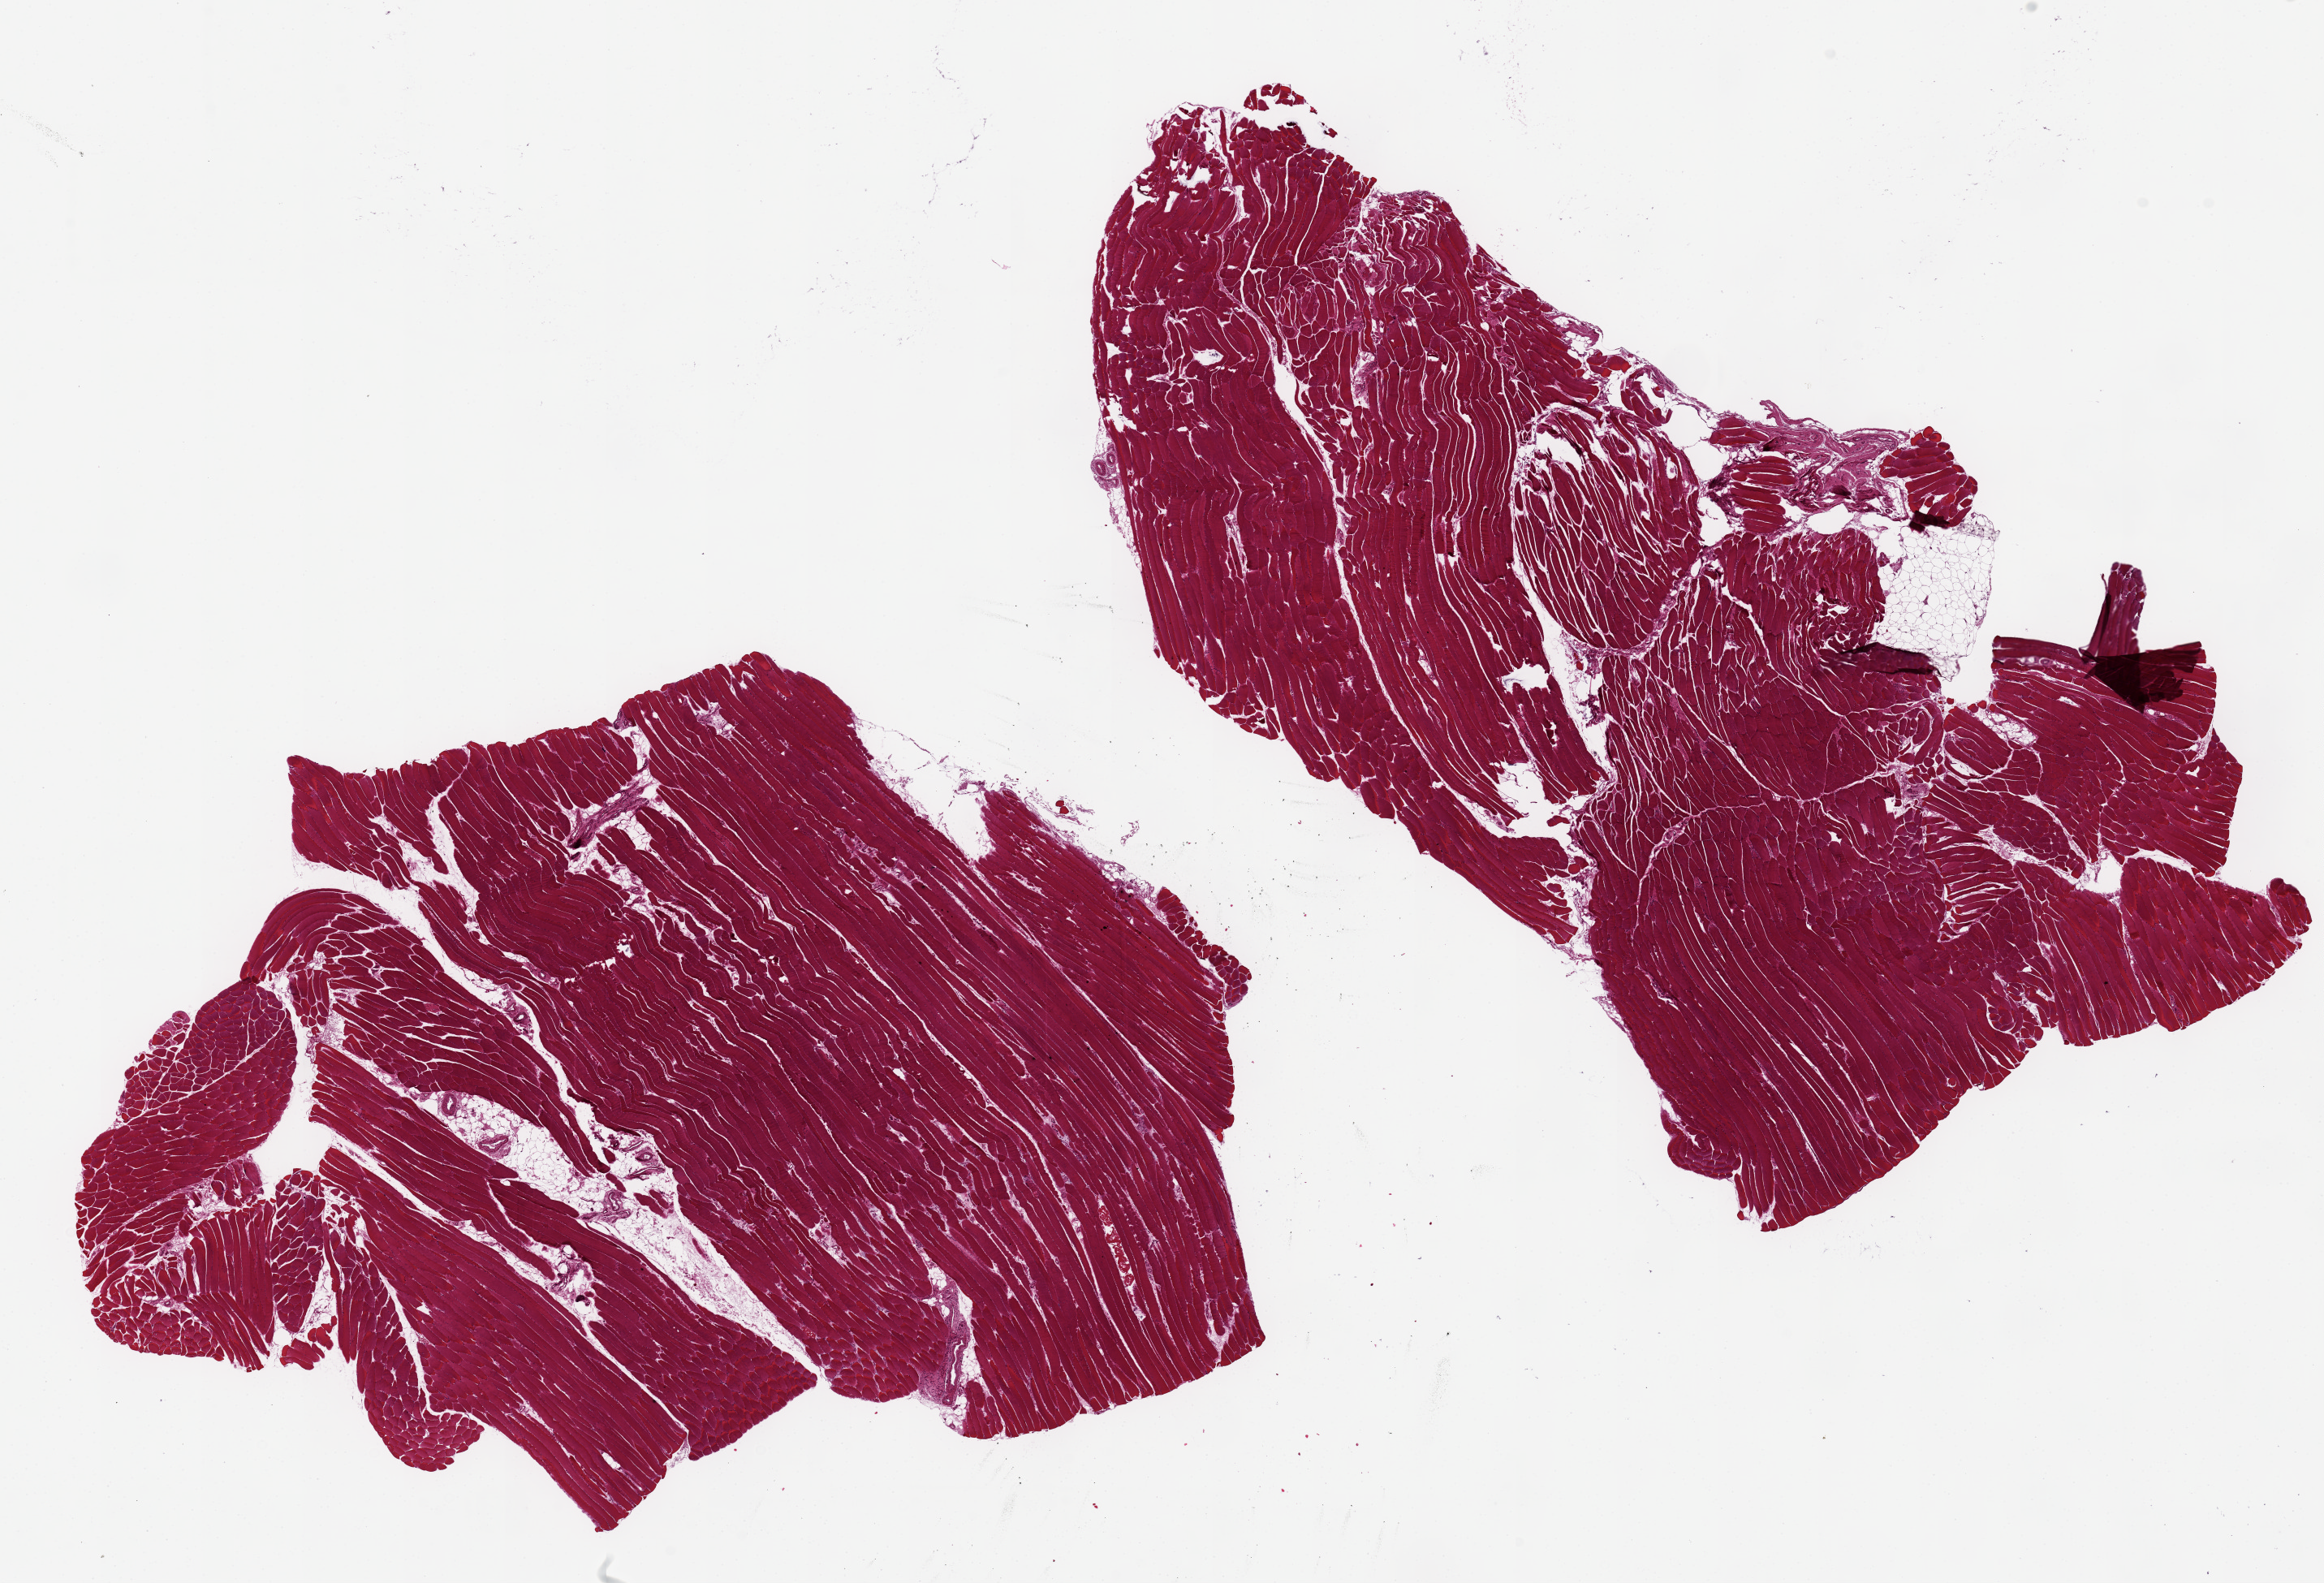
Whole-slide image, haematoxylin and eosin stain, whole scanned area (about 22.6 x 15.4 mm, from a 20x scan) shown as a low-resolution overview, PAXgene-fixed, paraffin-embedded tissue, sampled site (target tissue): skeletal muscle, donor tissue sample. Donor: male.
Review note (as recorded): 2 ~11x6mm aliquots, <5-10% interstitial fat.